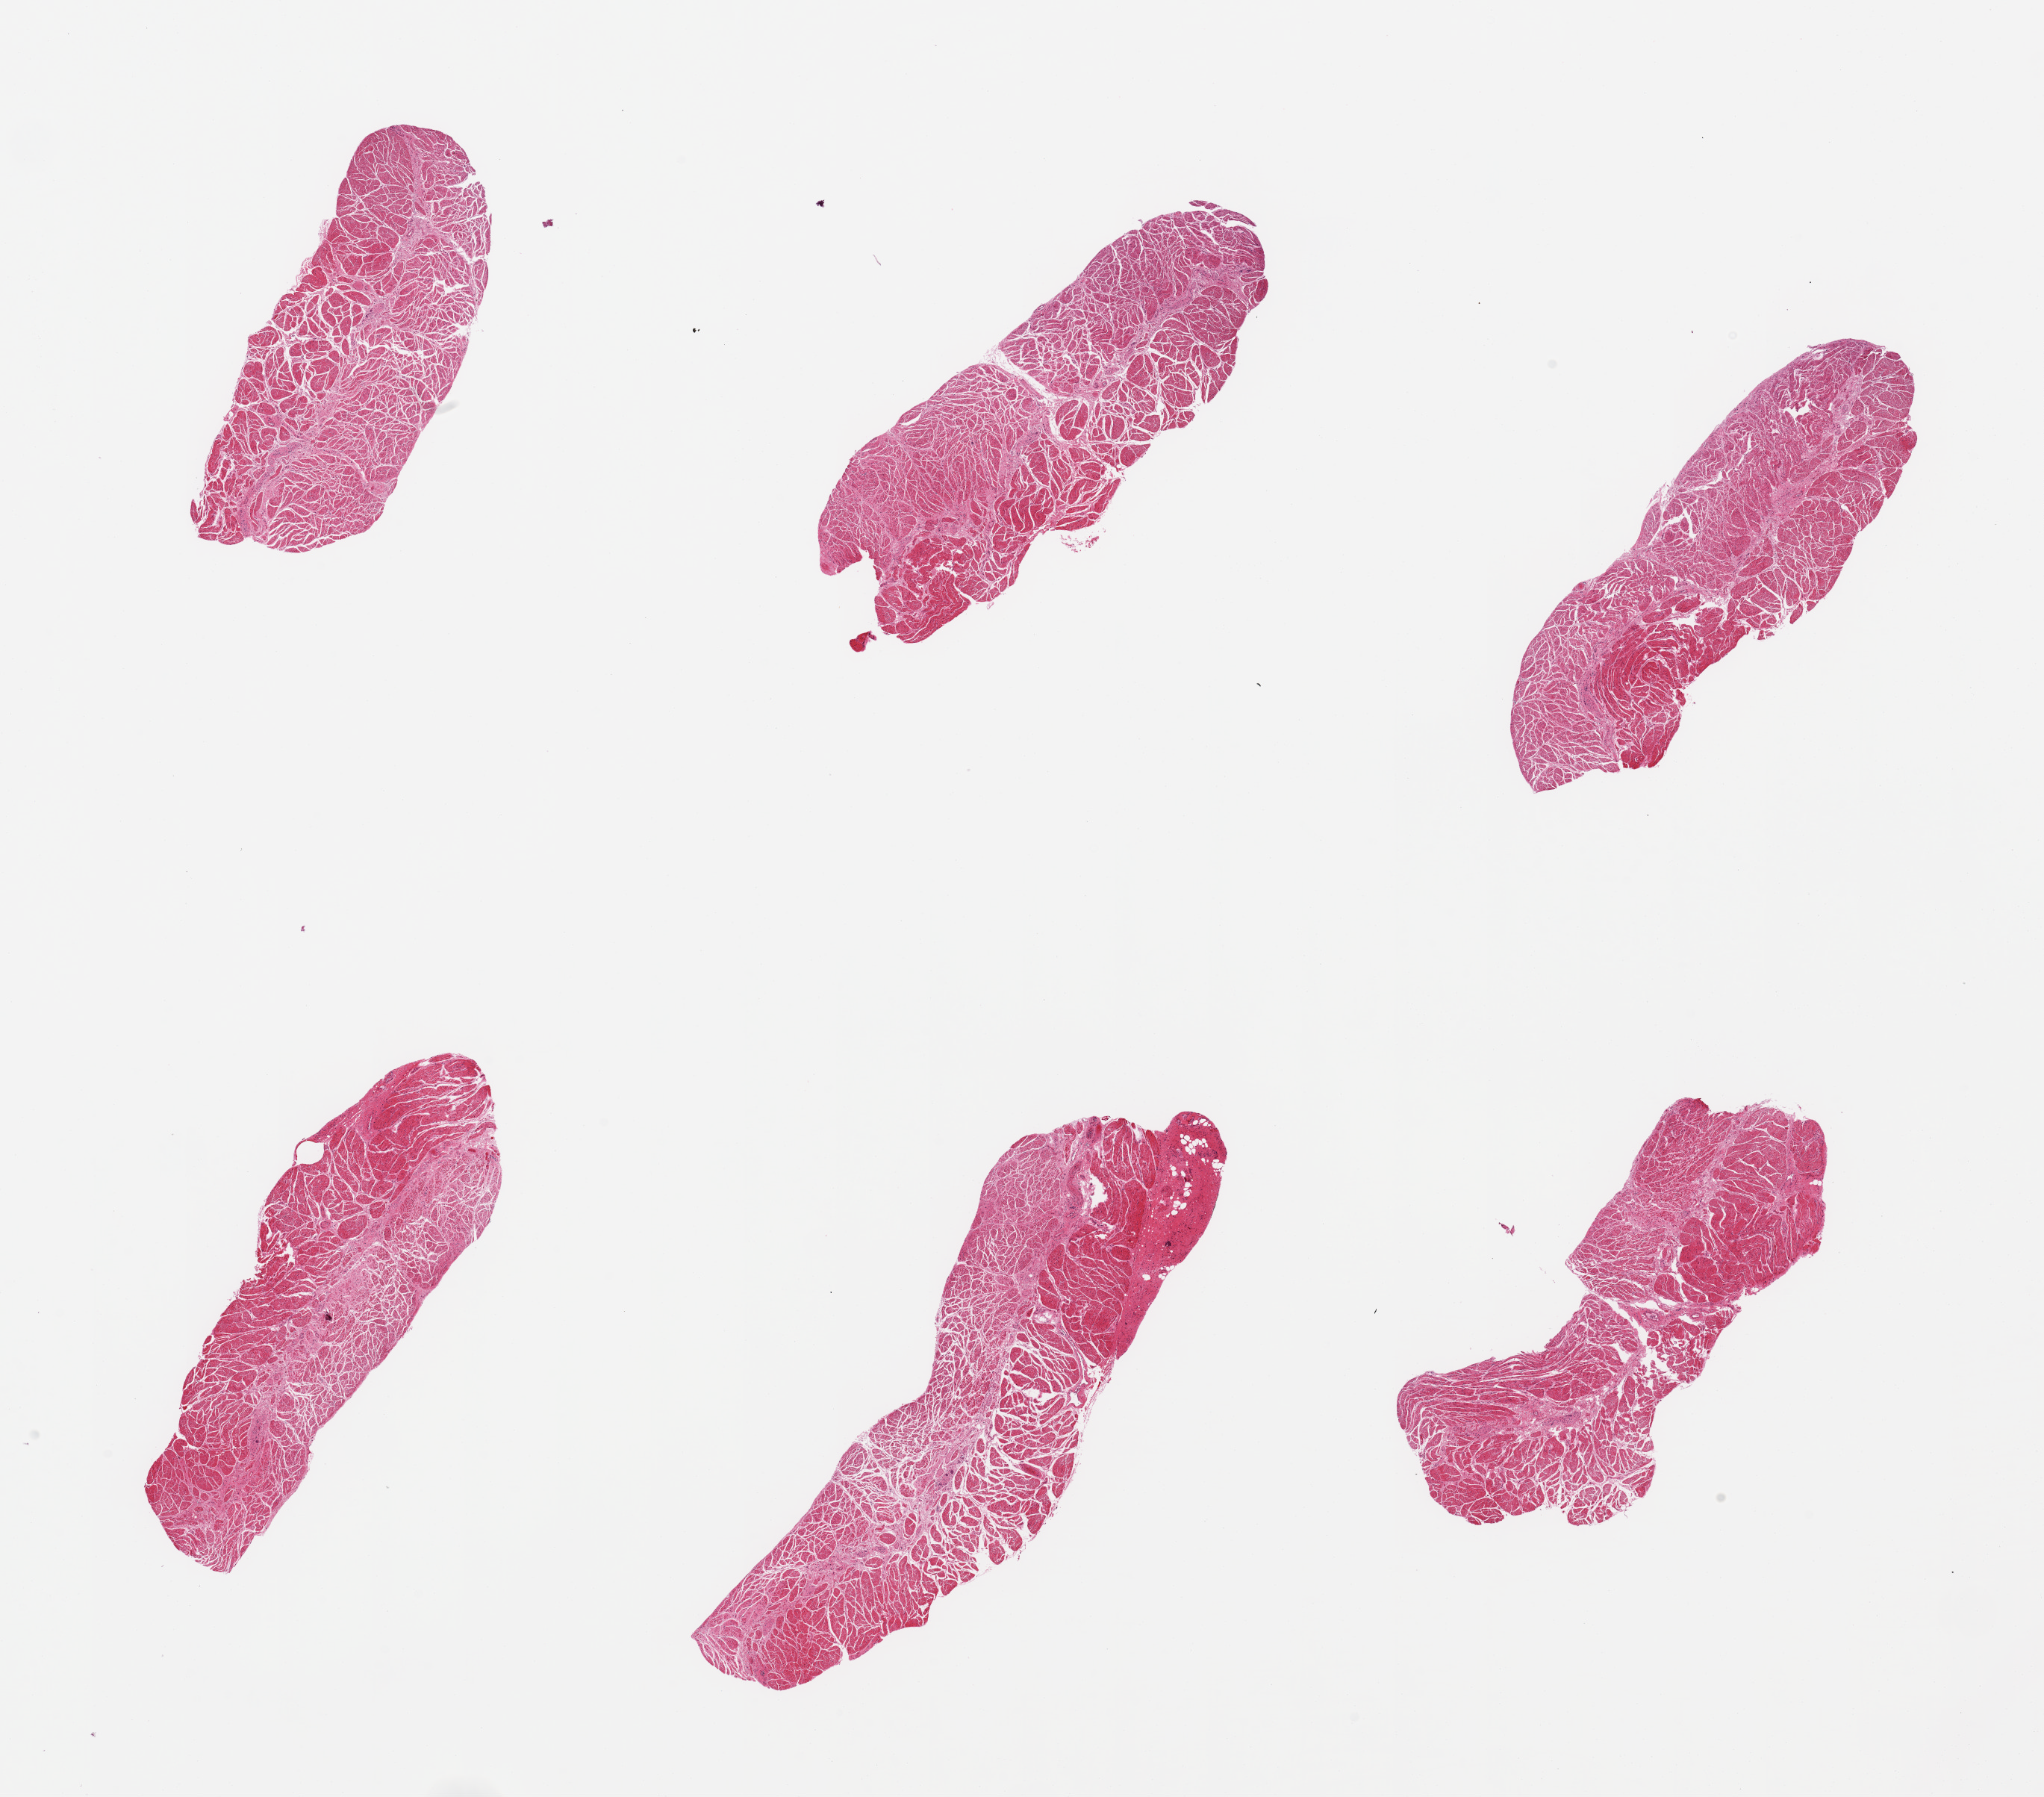
Whole-slide image, haematoxylin and eosin stain — shown as a low-resolution overview of the whole scanned area (about 21.7 x 19.0 mm), PAXgene-fixed paraffin-embedded (PFPE) section, section of gastroesophageal junction (target tissue), donor tissue sample. Donor sex: male.
Reviewer comment on this tissue sample: 6 pieces; scattered foci of fibrosis of muscle consistent with scleroderma.